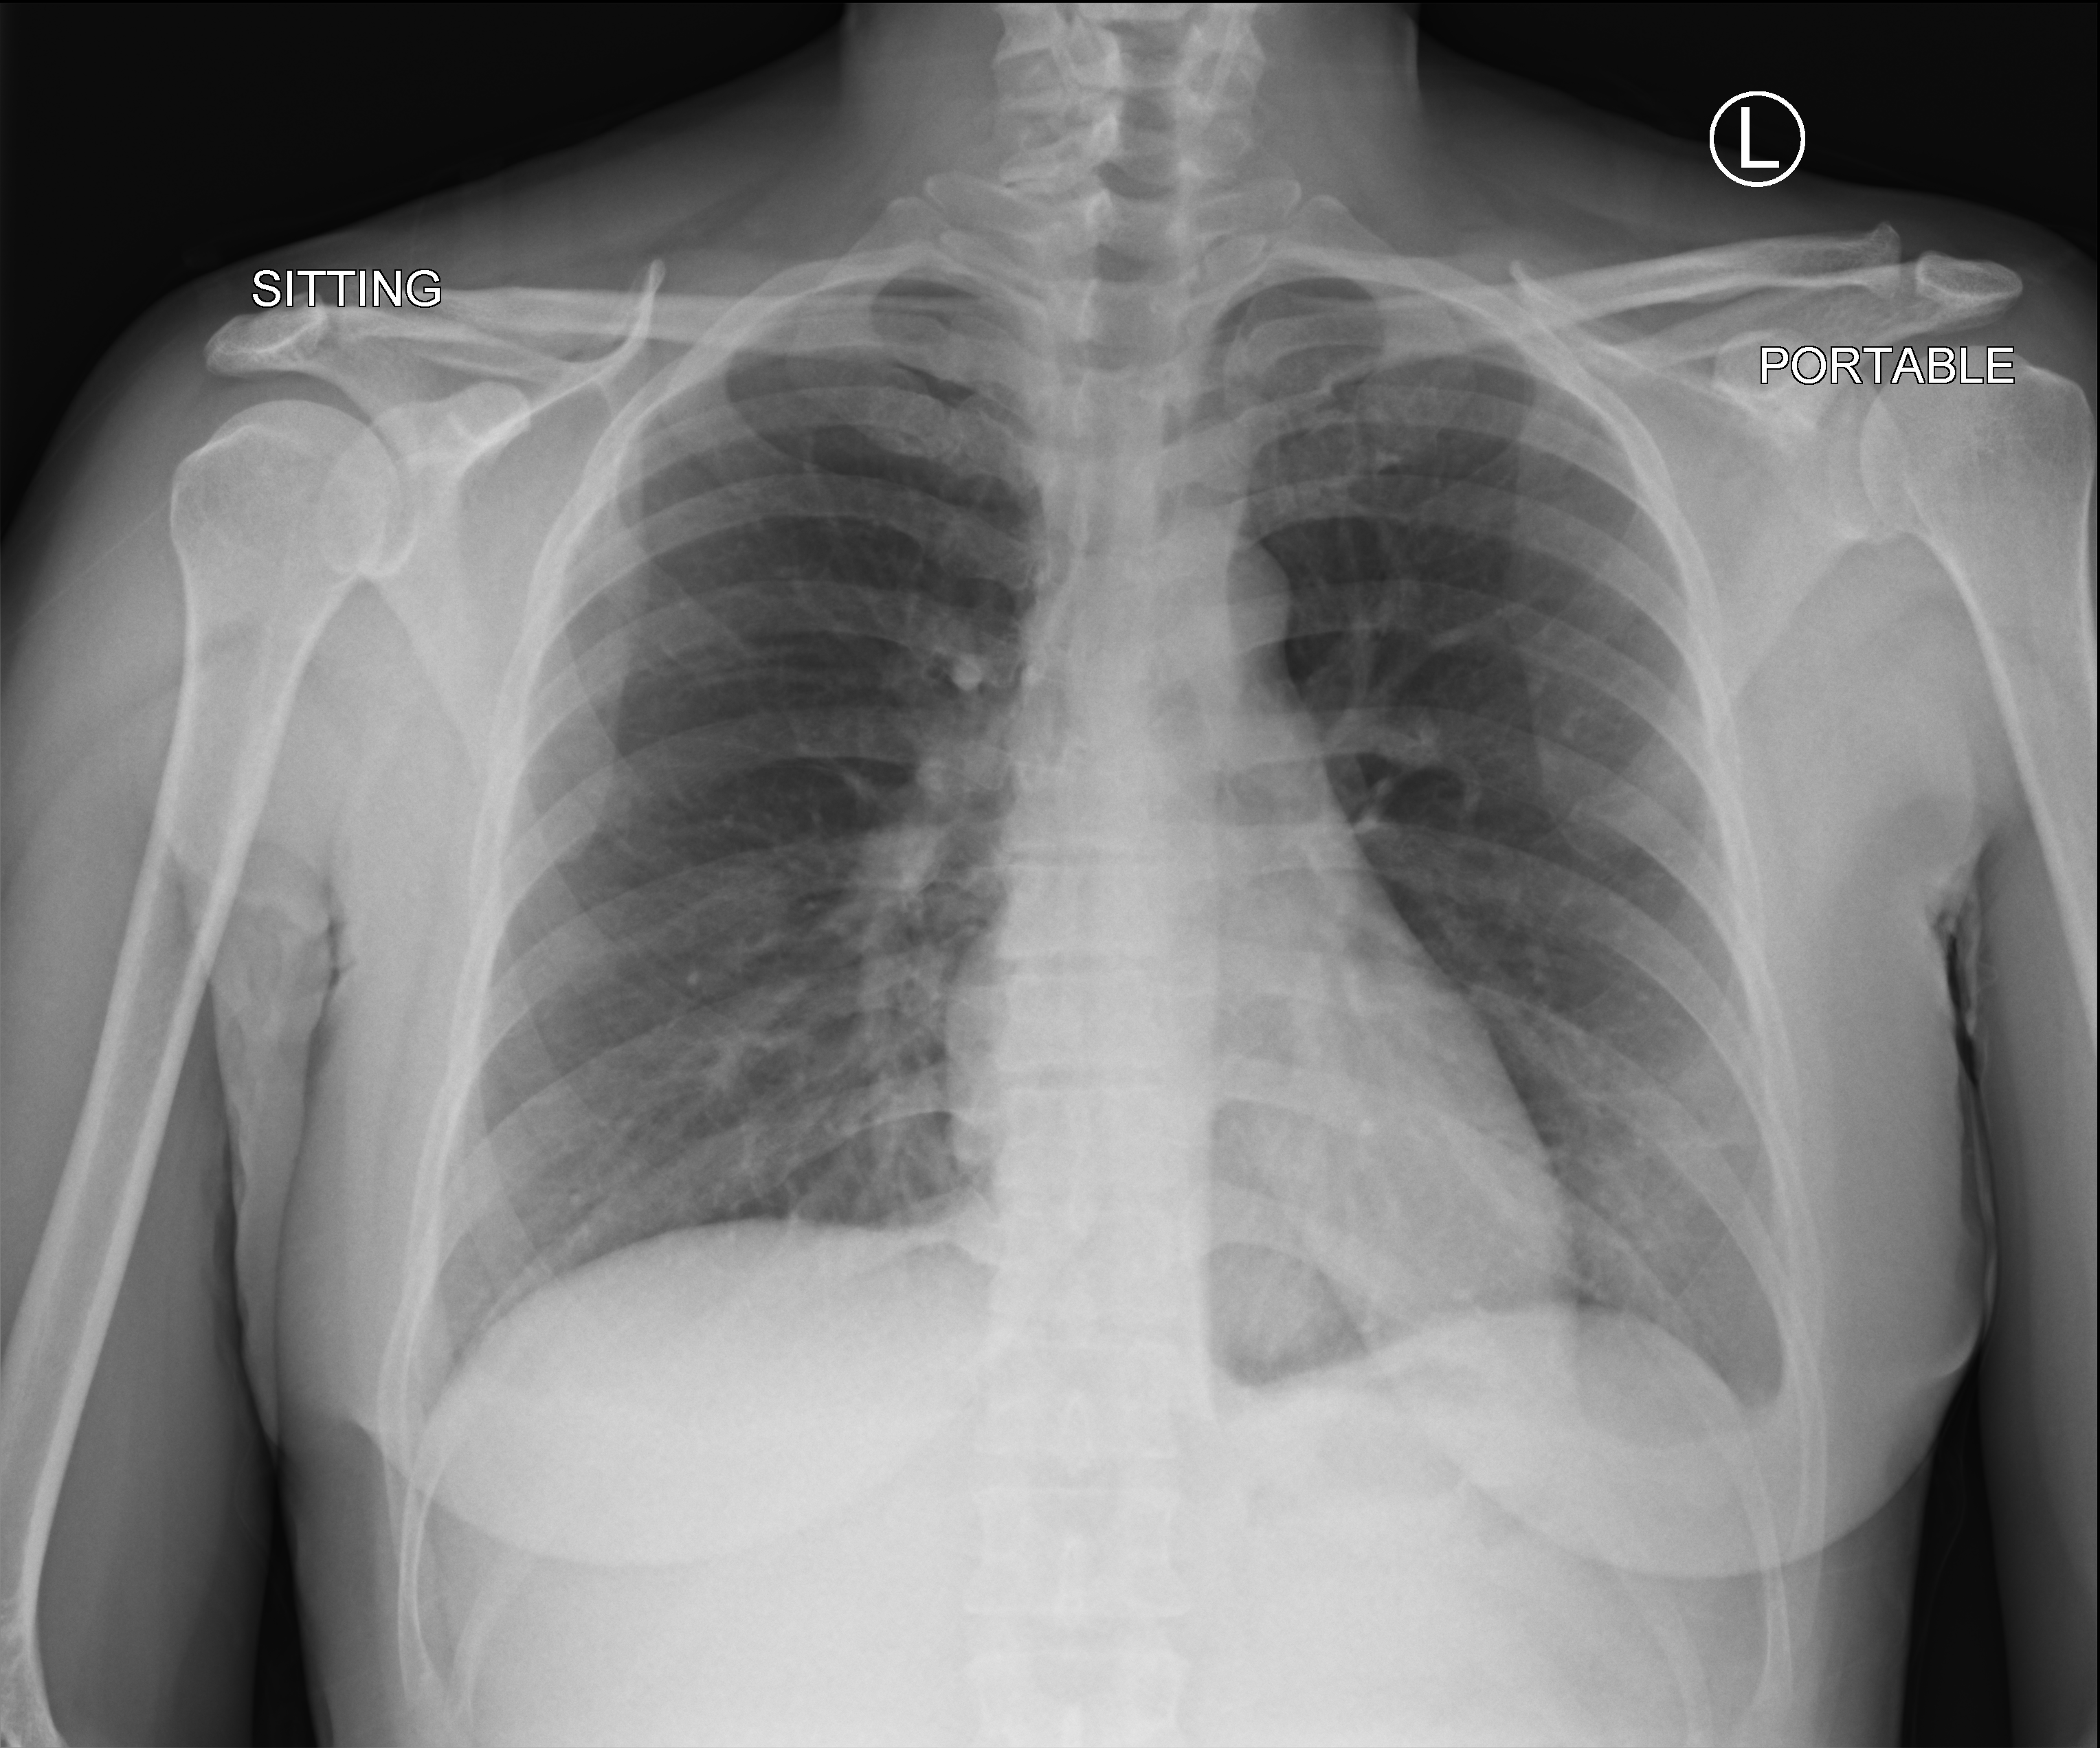
Bedside chest radiograph (computed radiography); anteroposterior (AP) projection. Female patient hospitalised with COVID-19, age 18–59 years.
Hospital-stay facts (about this admission, not read from this image; timing relative to this image not recorded): mechanically ventilated during this hospital stay: no; admitted to intensive care during this hospital stay: no; length of hospital stay: 1 day.